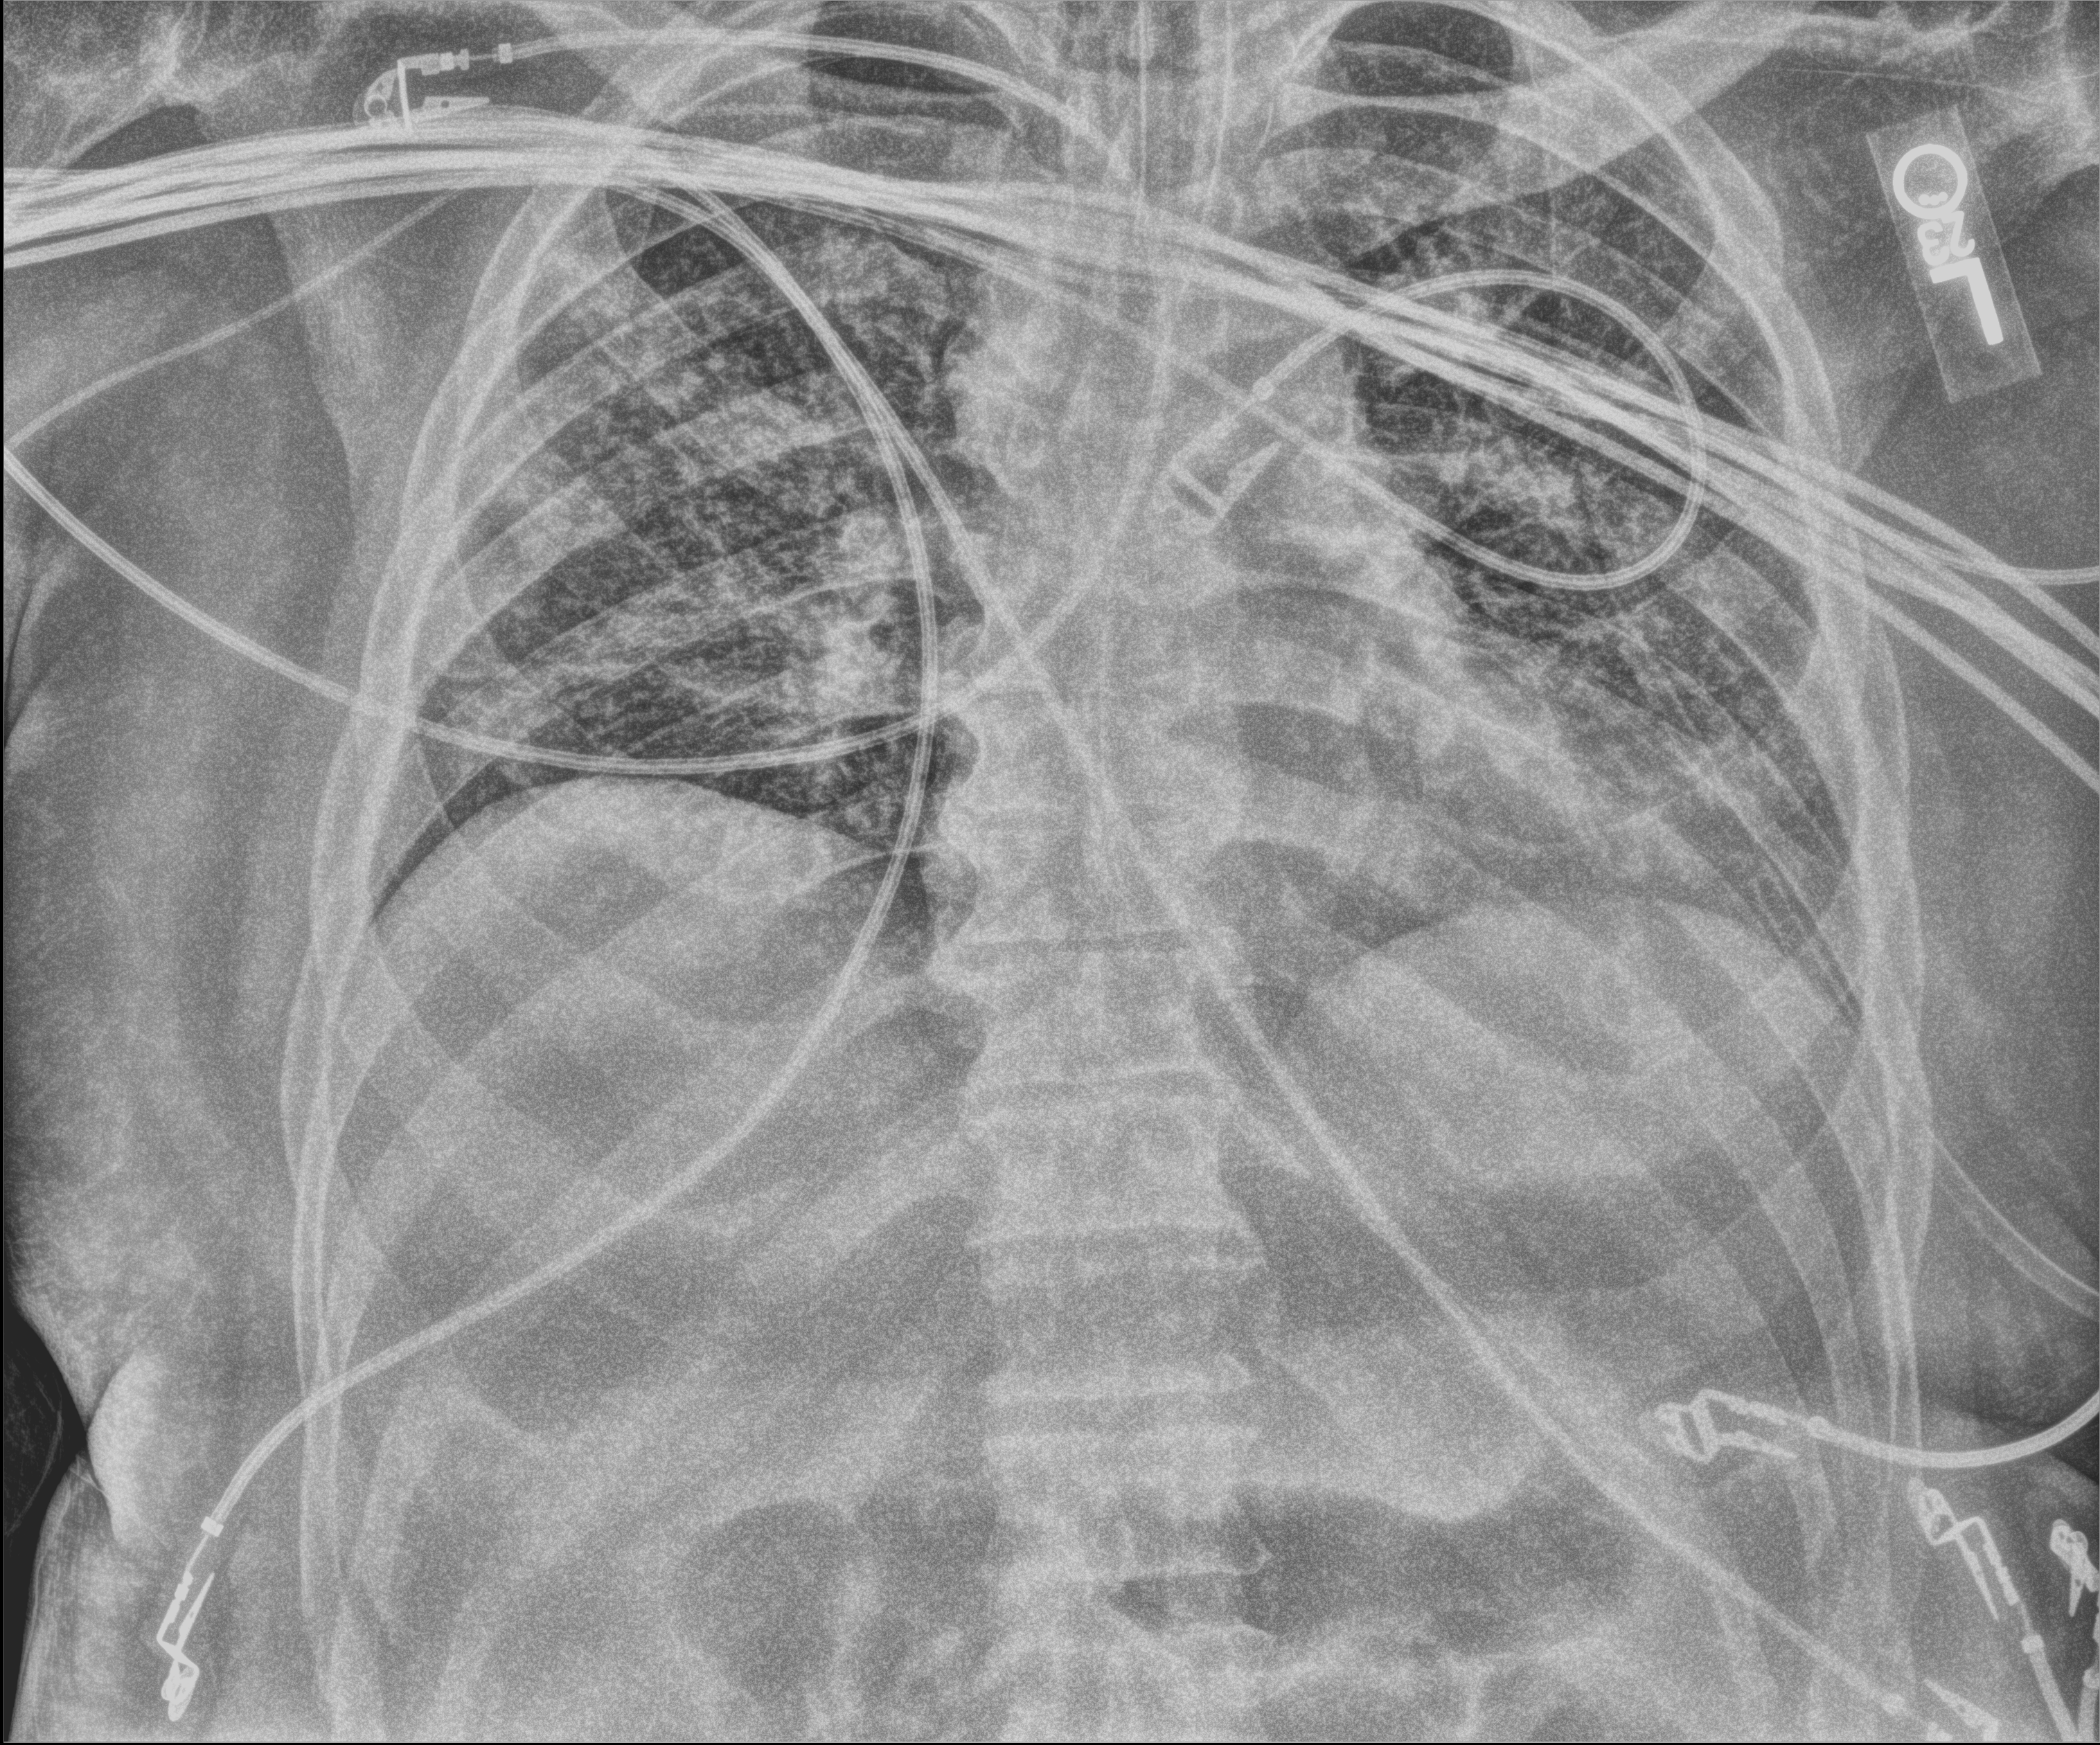
Chest X-ray (portable), anteroposterior (AP) projection. Male patient hospitalised with COVID-19, age 18–59 years.
Hospital-stay facts (about this admission, not read from this image; timing relative to this image not recorded):
- admitted to intensive care during this hospital stay: yes
- length of hospital stay: 41 days
- mechanically ventilated during this hospital stay: yes